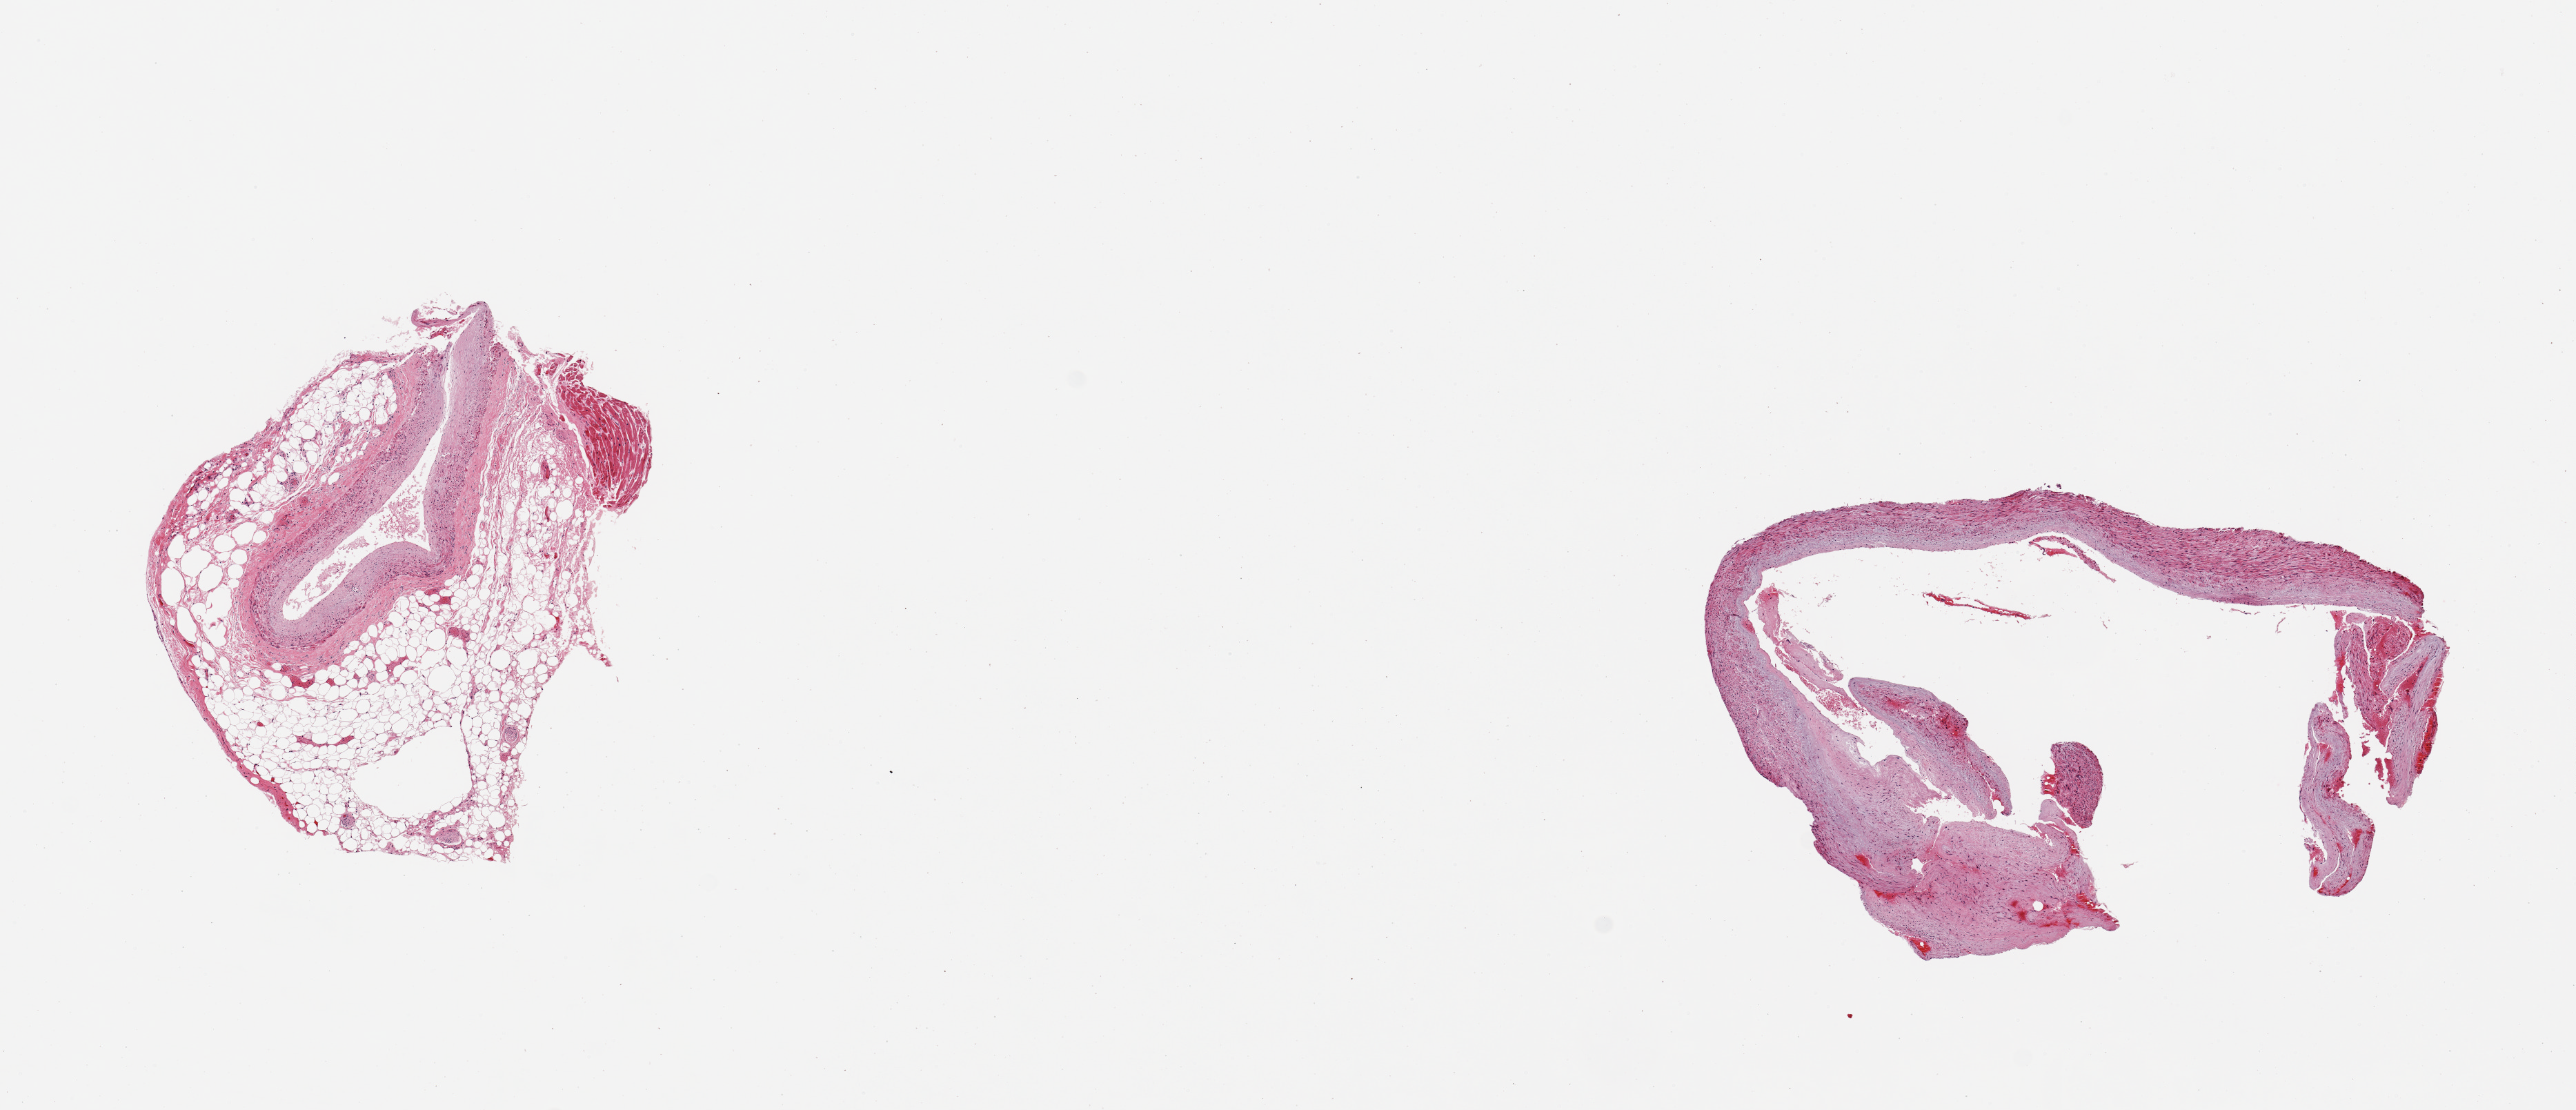
Digitized hematoxylin and eosin (H&E)-stained section, shown as a low-resolution overview of the whole scanned area (about 14.8 x 6.4 mm), PAXgene-fixed, paraffin-embedded tissue, target tissue: coronary artery, donor tissue sample. Male donor.
• review note (as recorded): 2 pieces; 1 with 60% fat and 10% myocardium; Other piece has fibrotic wall